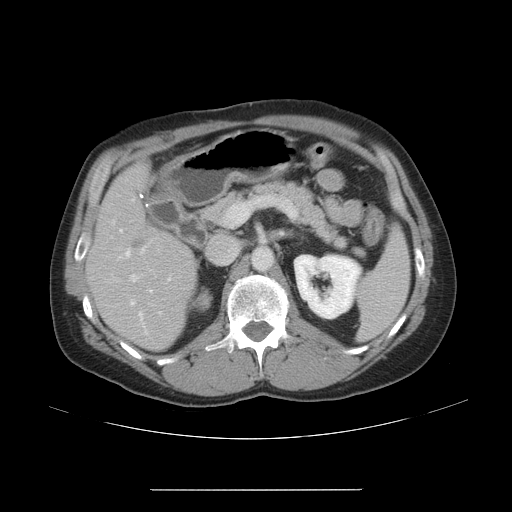
Contrast-enhanced abdominal CT, one axial slice; reconstruction kernel STANDARD; 120 kVp; intravenous contrast given; soft-tissue window (W 400 / L 40 HU); 5 mm slice thickness; 512 × 512 image matrix. Male patient, age 56 years. Case-level facts recorded for this patient, not image findings: diagnosis: colorectal cancer liver metastases, imaged before liver resection; multiple liver metastases: yes; largest metastasis: 1.8 cm; chemotherapy before resection: yes.
Outlined on this slice (outlined manually by an expert reader):
- hepatic veins: box from (x=117, y=245) to (x=153, y=335) px
- liver: (x=88, y=168)–(x=197, y=349)
- planned liver remnant (the part of the liver to remain after resection): (x=91, y=168)–(x=197, y=349)
- portal vein (with intrahepatic branches): (x=119, y=229)–(x=139, y=282)
- liver metastasis: (x=134, y=240)–(x=144, y=248)